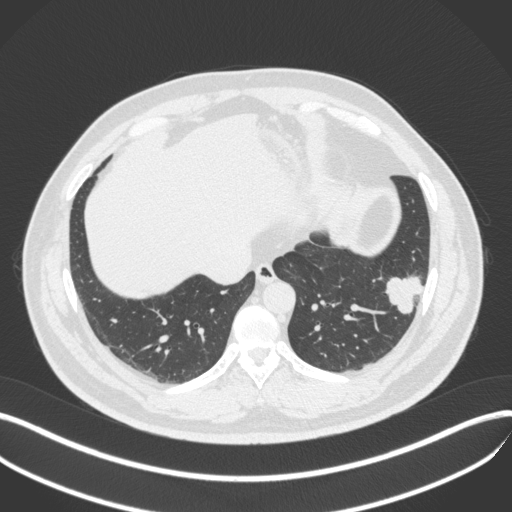
Chest CT, one axial slice. Position 121 of 420 along the scan axis. Reconstruction kernel B31f. 120 kVp. Lung window (W 1500 / L -600 HU). 1 mm slice thickness. 512 × 512 image matrix, field of view 400 × 400 mm. Male patient, age 39 years. From the clinical record (not read from this slice): clinical TNM (as recorded): T2a N0 M0; histopathological grade: G2-3.
Outlined on this slice (bounding box drawn by a radiologist):
- lung tumour (recorded histology: adenocarcinoma): box from (x=380, y=269) to (x=426, y=320) px